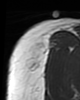
MRI of an extremity soft-tissue mass, one axial slice; slice 33 of 46 in the series (ordered by position); MR volume resampled by the dataset authors to the PET/CT grid (not the native acquisition matrix); 3.27 mm slice thickness; 80 × 100 image matrix, field of view 78 × 98 mm. Female patient. Case-level facts recorded for this patient, not image findings: histological type: synovial sarcoma; grade: intermediate; site of the primary tumour: right thigh.
Annotated regions visible in this slice (expert contour drawn on MRI and transferred to this co-registered scan by the dataset authors):
- gross tumour volume including surrounding oedema: box from (x=28, y=46) to (x=45, y=72) px
- gross tumour volume (mass): (x=28, y=51)–(x=42, y=72)